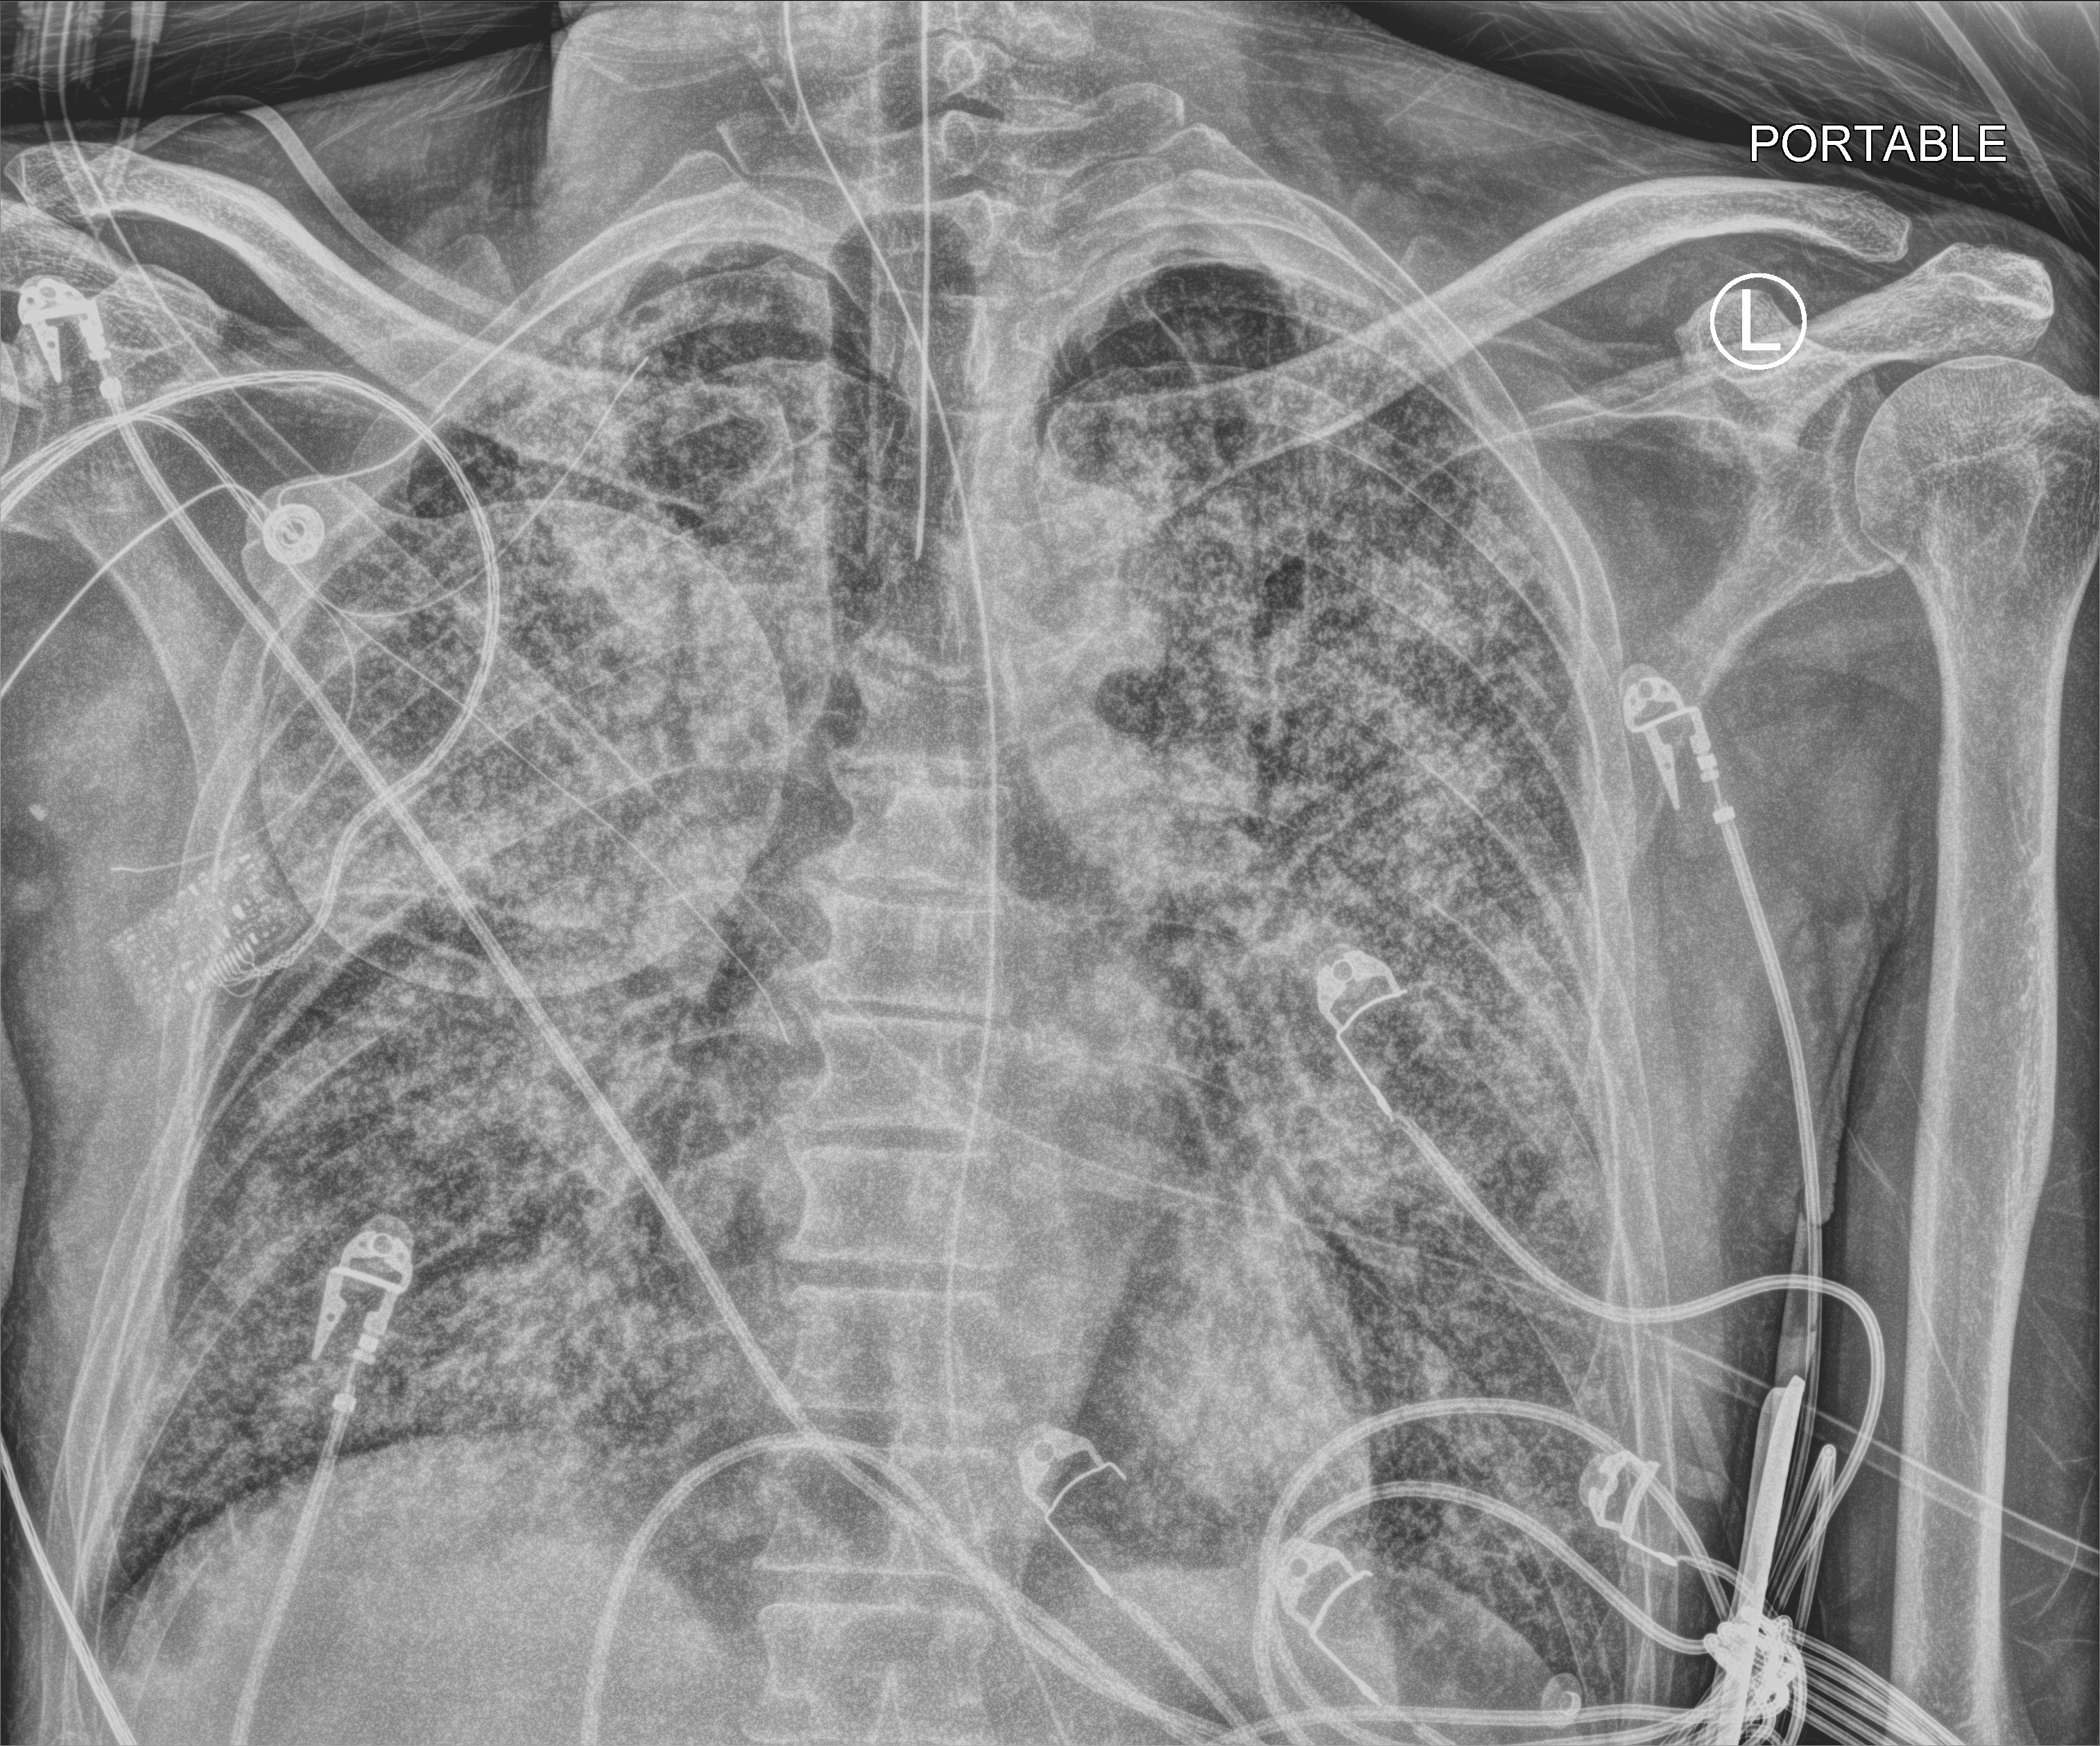
Chest X-ray (portable), anteroposterior (AP) projection. Patient hospitalised with COVID-19; male, aged 60–74 years.
From the hospital-stay record, not from the radiograph (when in the stay this image was taken is not recorded): chronic kidney disease (admission record): no; admitted to intensive care during this hospital stay: yes; length of hospital stay: 3 days.